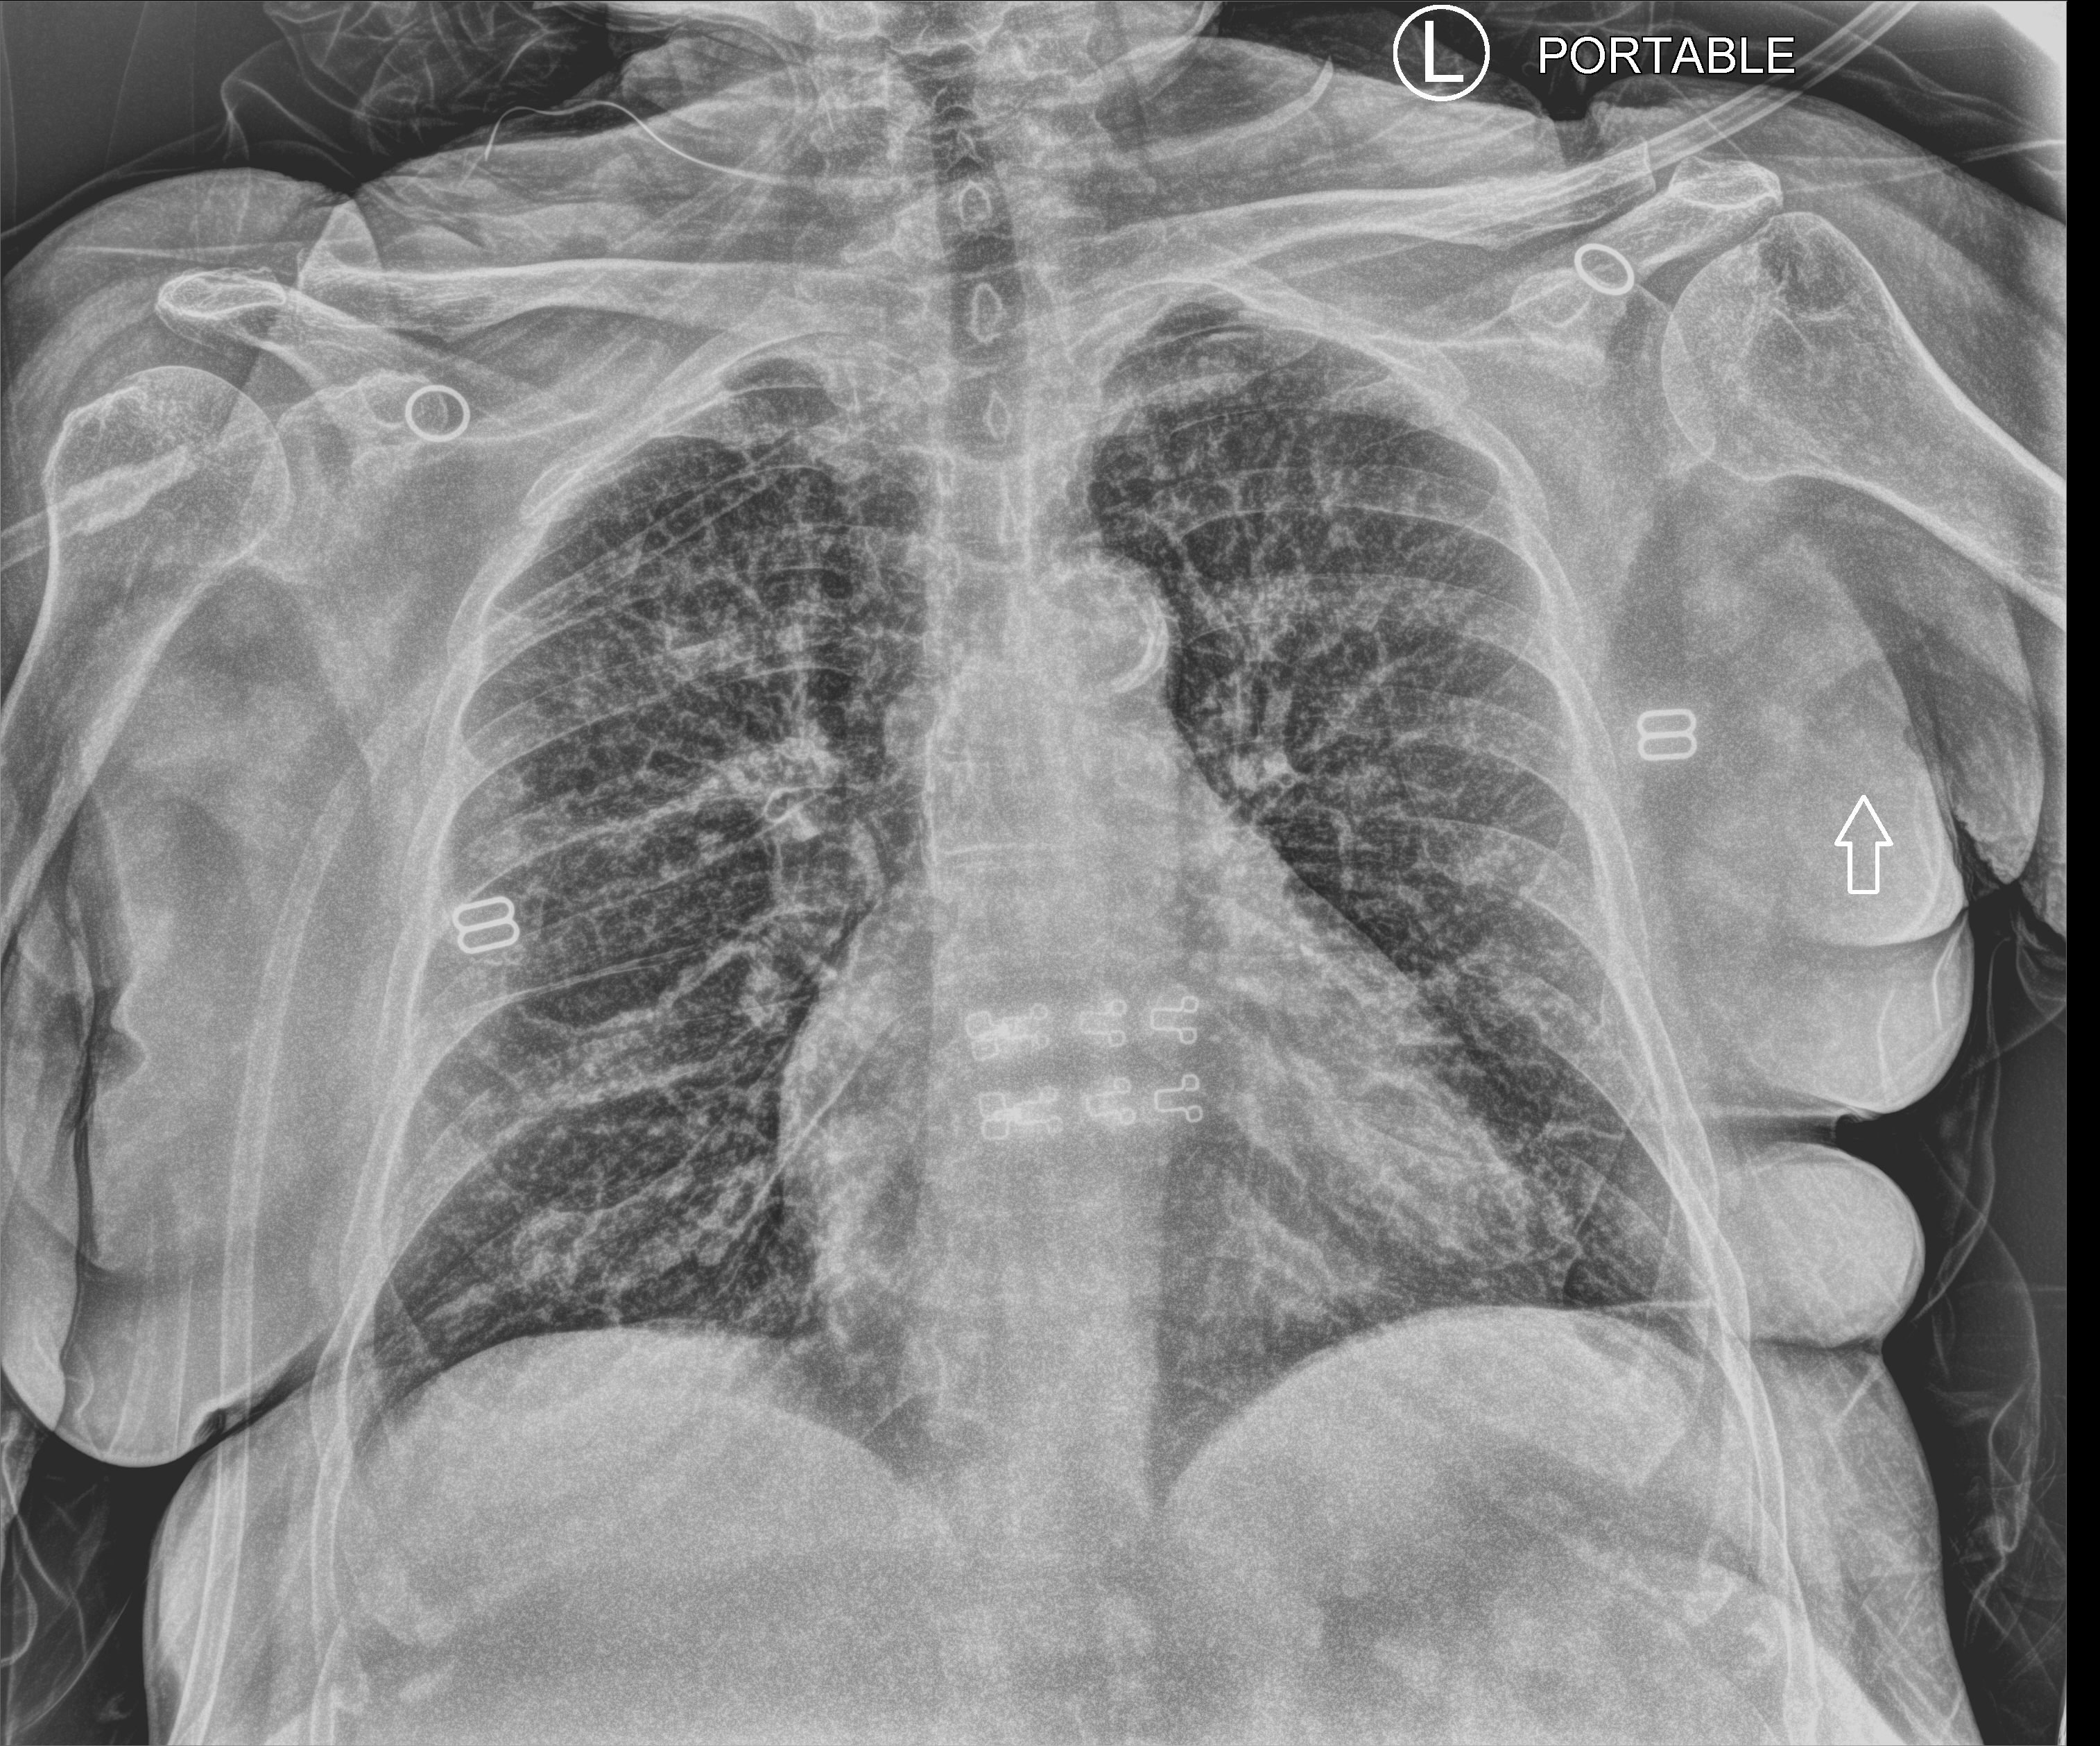
Portable chest radiograph, anteroposterior (AP) projection. Female patient hospitalised with COVID-19, age 75–90 years.
Admission-level facts for this patient (not findings on this image; timing relative to this image not recorded): length of hospital stay: 1 day; admitted to intensive care during this hospital stay: no.